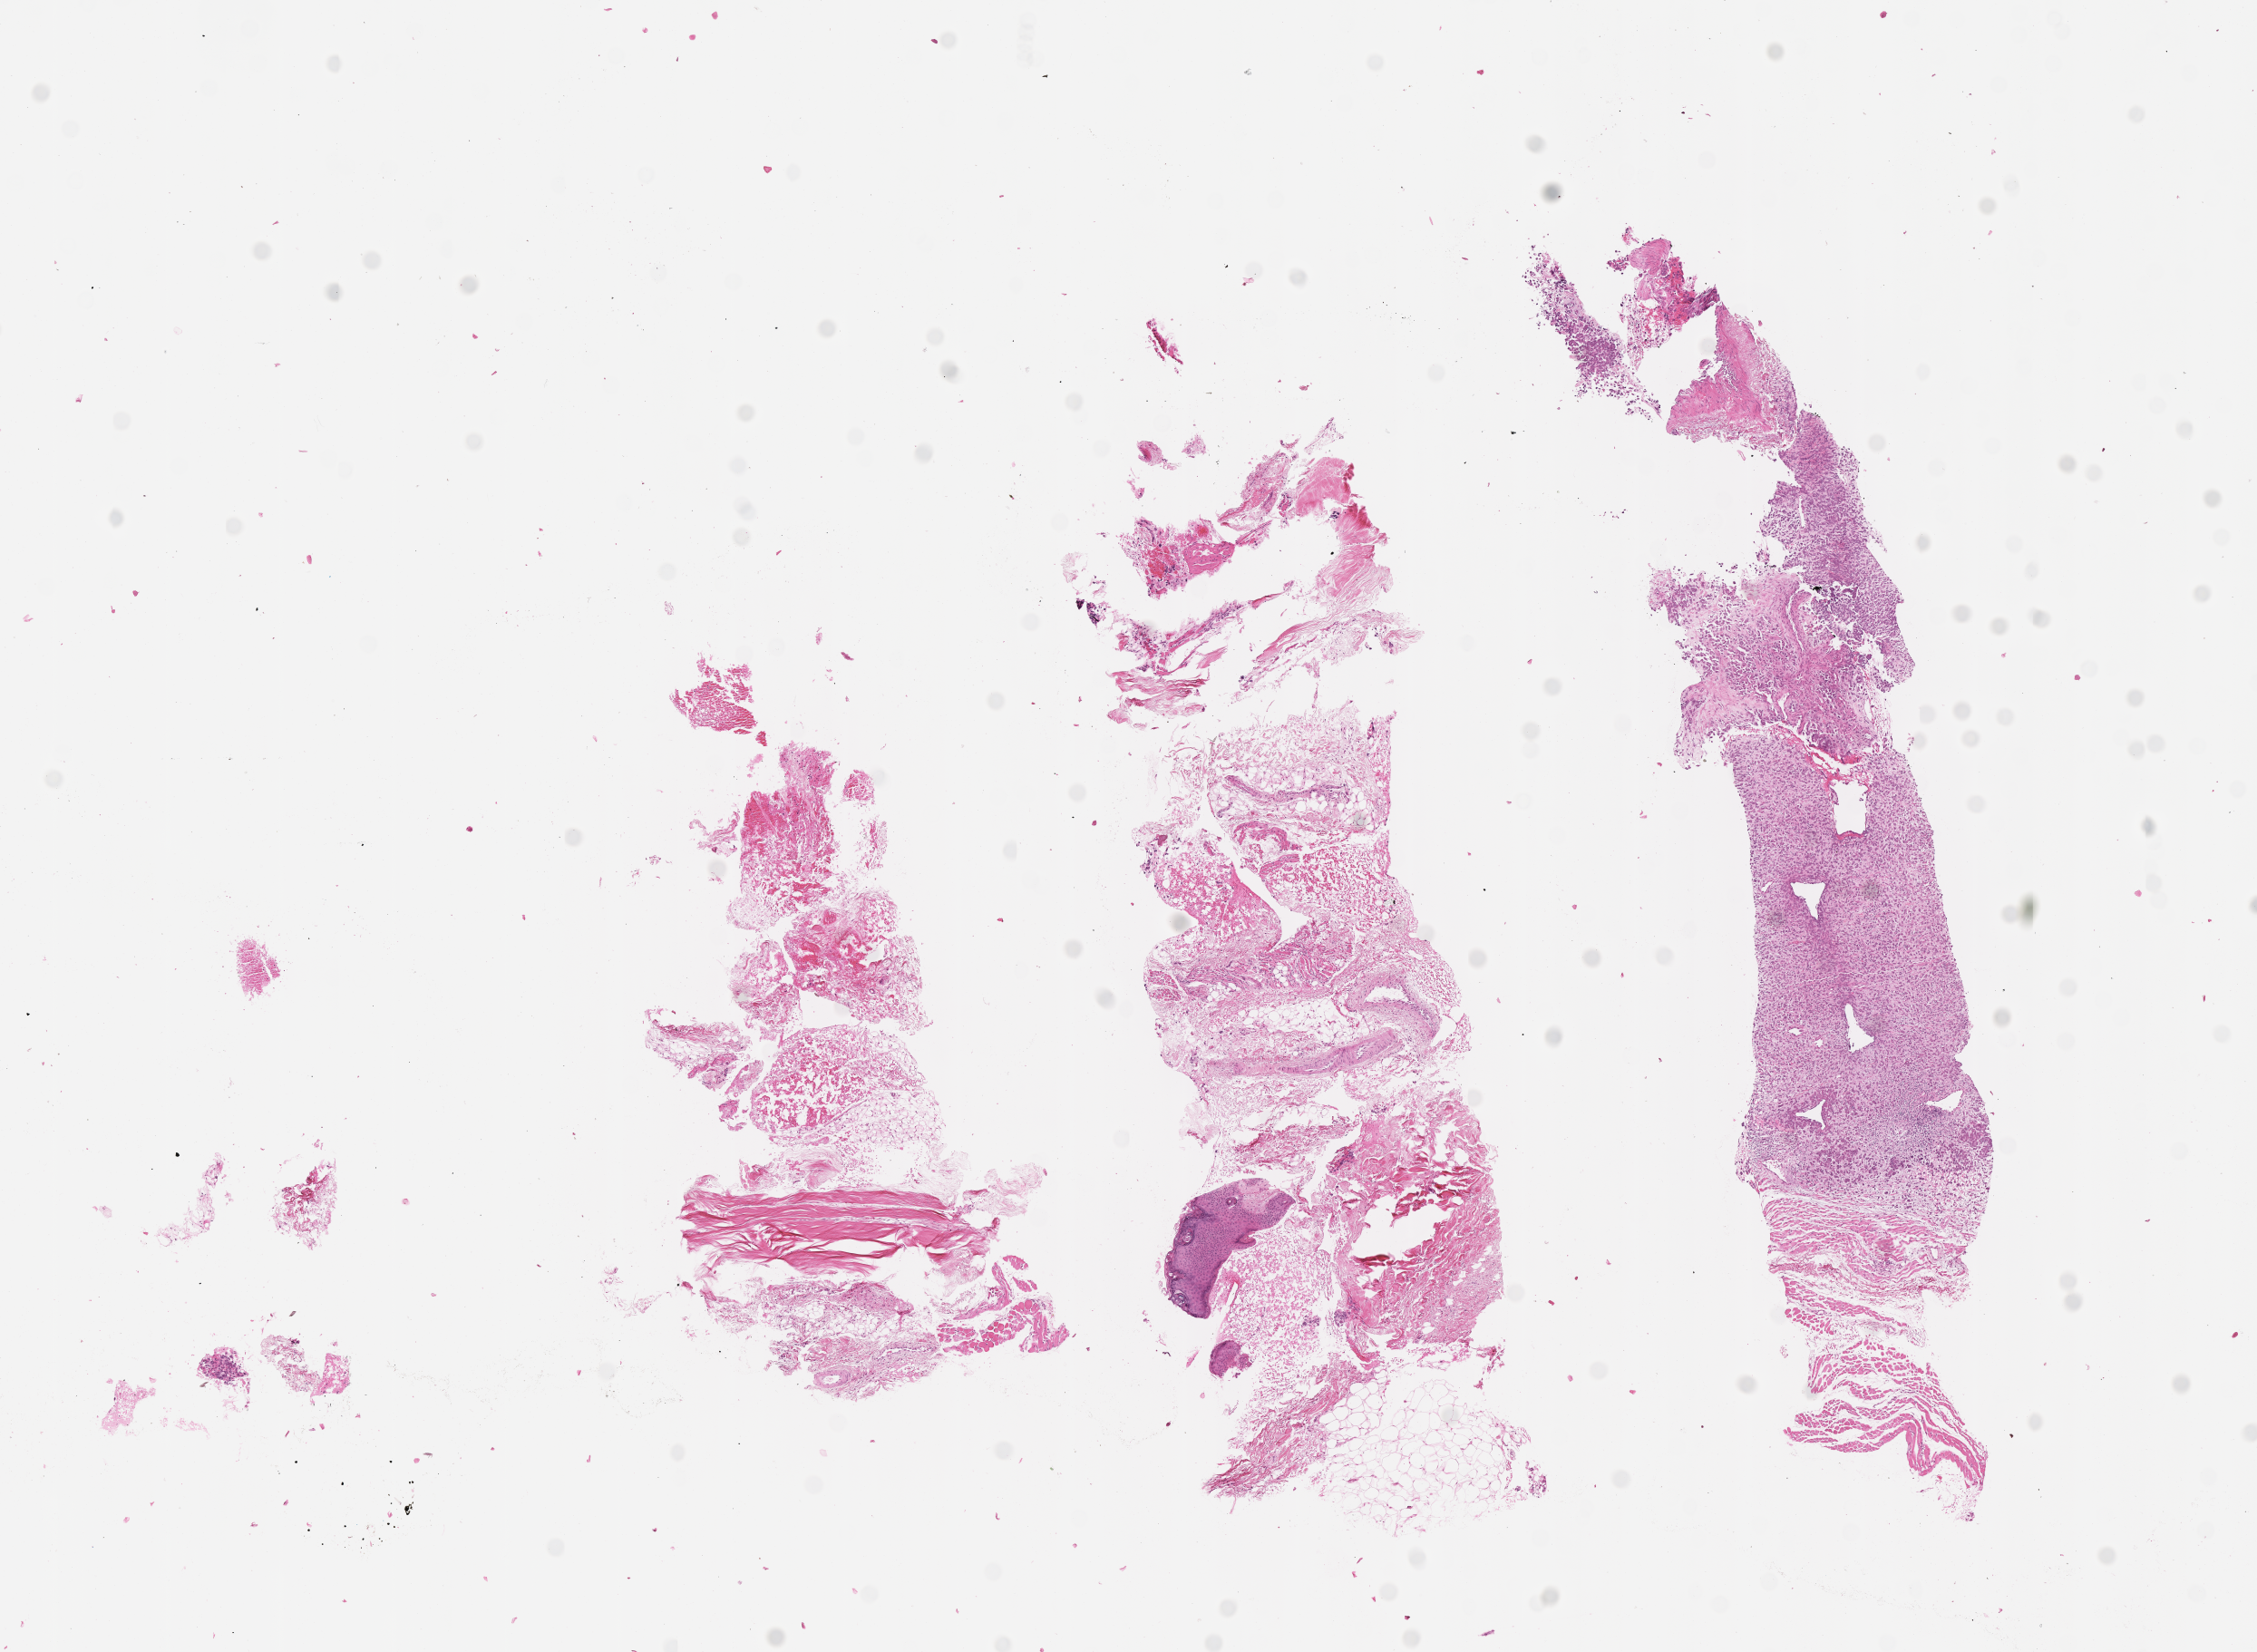
Digitized haematoxylin and eosin-stained section of tumor tissue — whole scanned area (about 10.1 x 7.4 mm) shown as a low-resolution overview; formalin-fixed, paraffin-embedded (FFPE) tissue; site: soft tissue, face/head-left. Patient: male, age 4.1 years at diagnosis.
Diagnosis: rhabdomyosarcoma; histological classification: embryonal rhabdomyosarcoma.